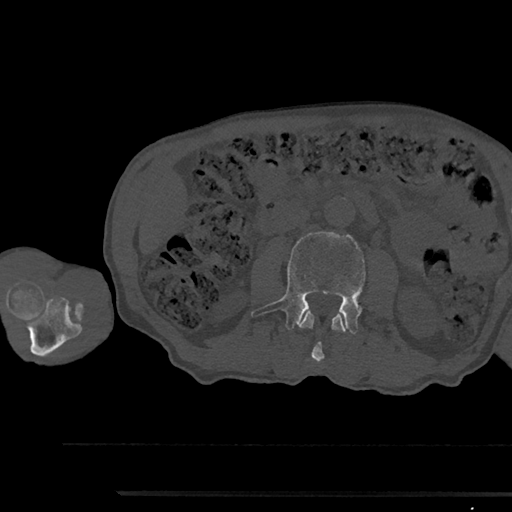
CT including the spine, one axial slice; slice 514 of 797 in the series (ordered by position); 120 kVp; bone window (W 1800 / L 400 HU); 0.5 mm slice thickness; 512 × 512 image matrix, field of view 367 × 367 mm. Male patient, age 79 years. From the clinical record (not read from this slice): primary cancer: prostate.
Annotated regions visible in this slice (semi-automatic segmentation, software-assisted and operator-edited):
- L2 vertebra: bounding box (x1, y1, x2, y2) in pixels: (298, 310, 347, 362)
- L3 vertebra: (251, 232, 372, 334)